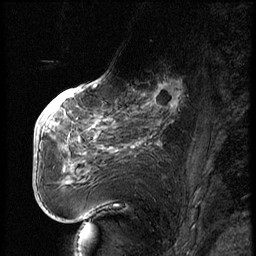
Breast MRI (dynamic contrast-enhanced), one sagittal slice; slice 28 of 74 in the series (ordered by position); dynamic contrast-enhanced series, image 2 of 3 at this slice position (ordered by acquisition); 1.5 T; TE 4.2 ms, TR 9 ms; 2.5 mm slice thickness; 256 × 256 image matrix, field of view 180 × 180 mm. Female patient, age 56 years. Case-level facts recorded for this patient, not image findings: setting: breast cancer imaged before/during neoadjuvant chemotherapy.
Outlined on this slice (semi-automatic segmentation, software-assisted and operator-edited):
- analysis volume of interest (the breast-tissue region the enhancement analysis was run in; not a lesion): bounding box (x1, y1, x2, y2) in pixels: (123, 71, 195, 131)
- tumour enhancement mask (voxels above the 140 % enhancement threshold inside the analysis volume of interest): (151, 79, 183, 113)